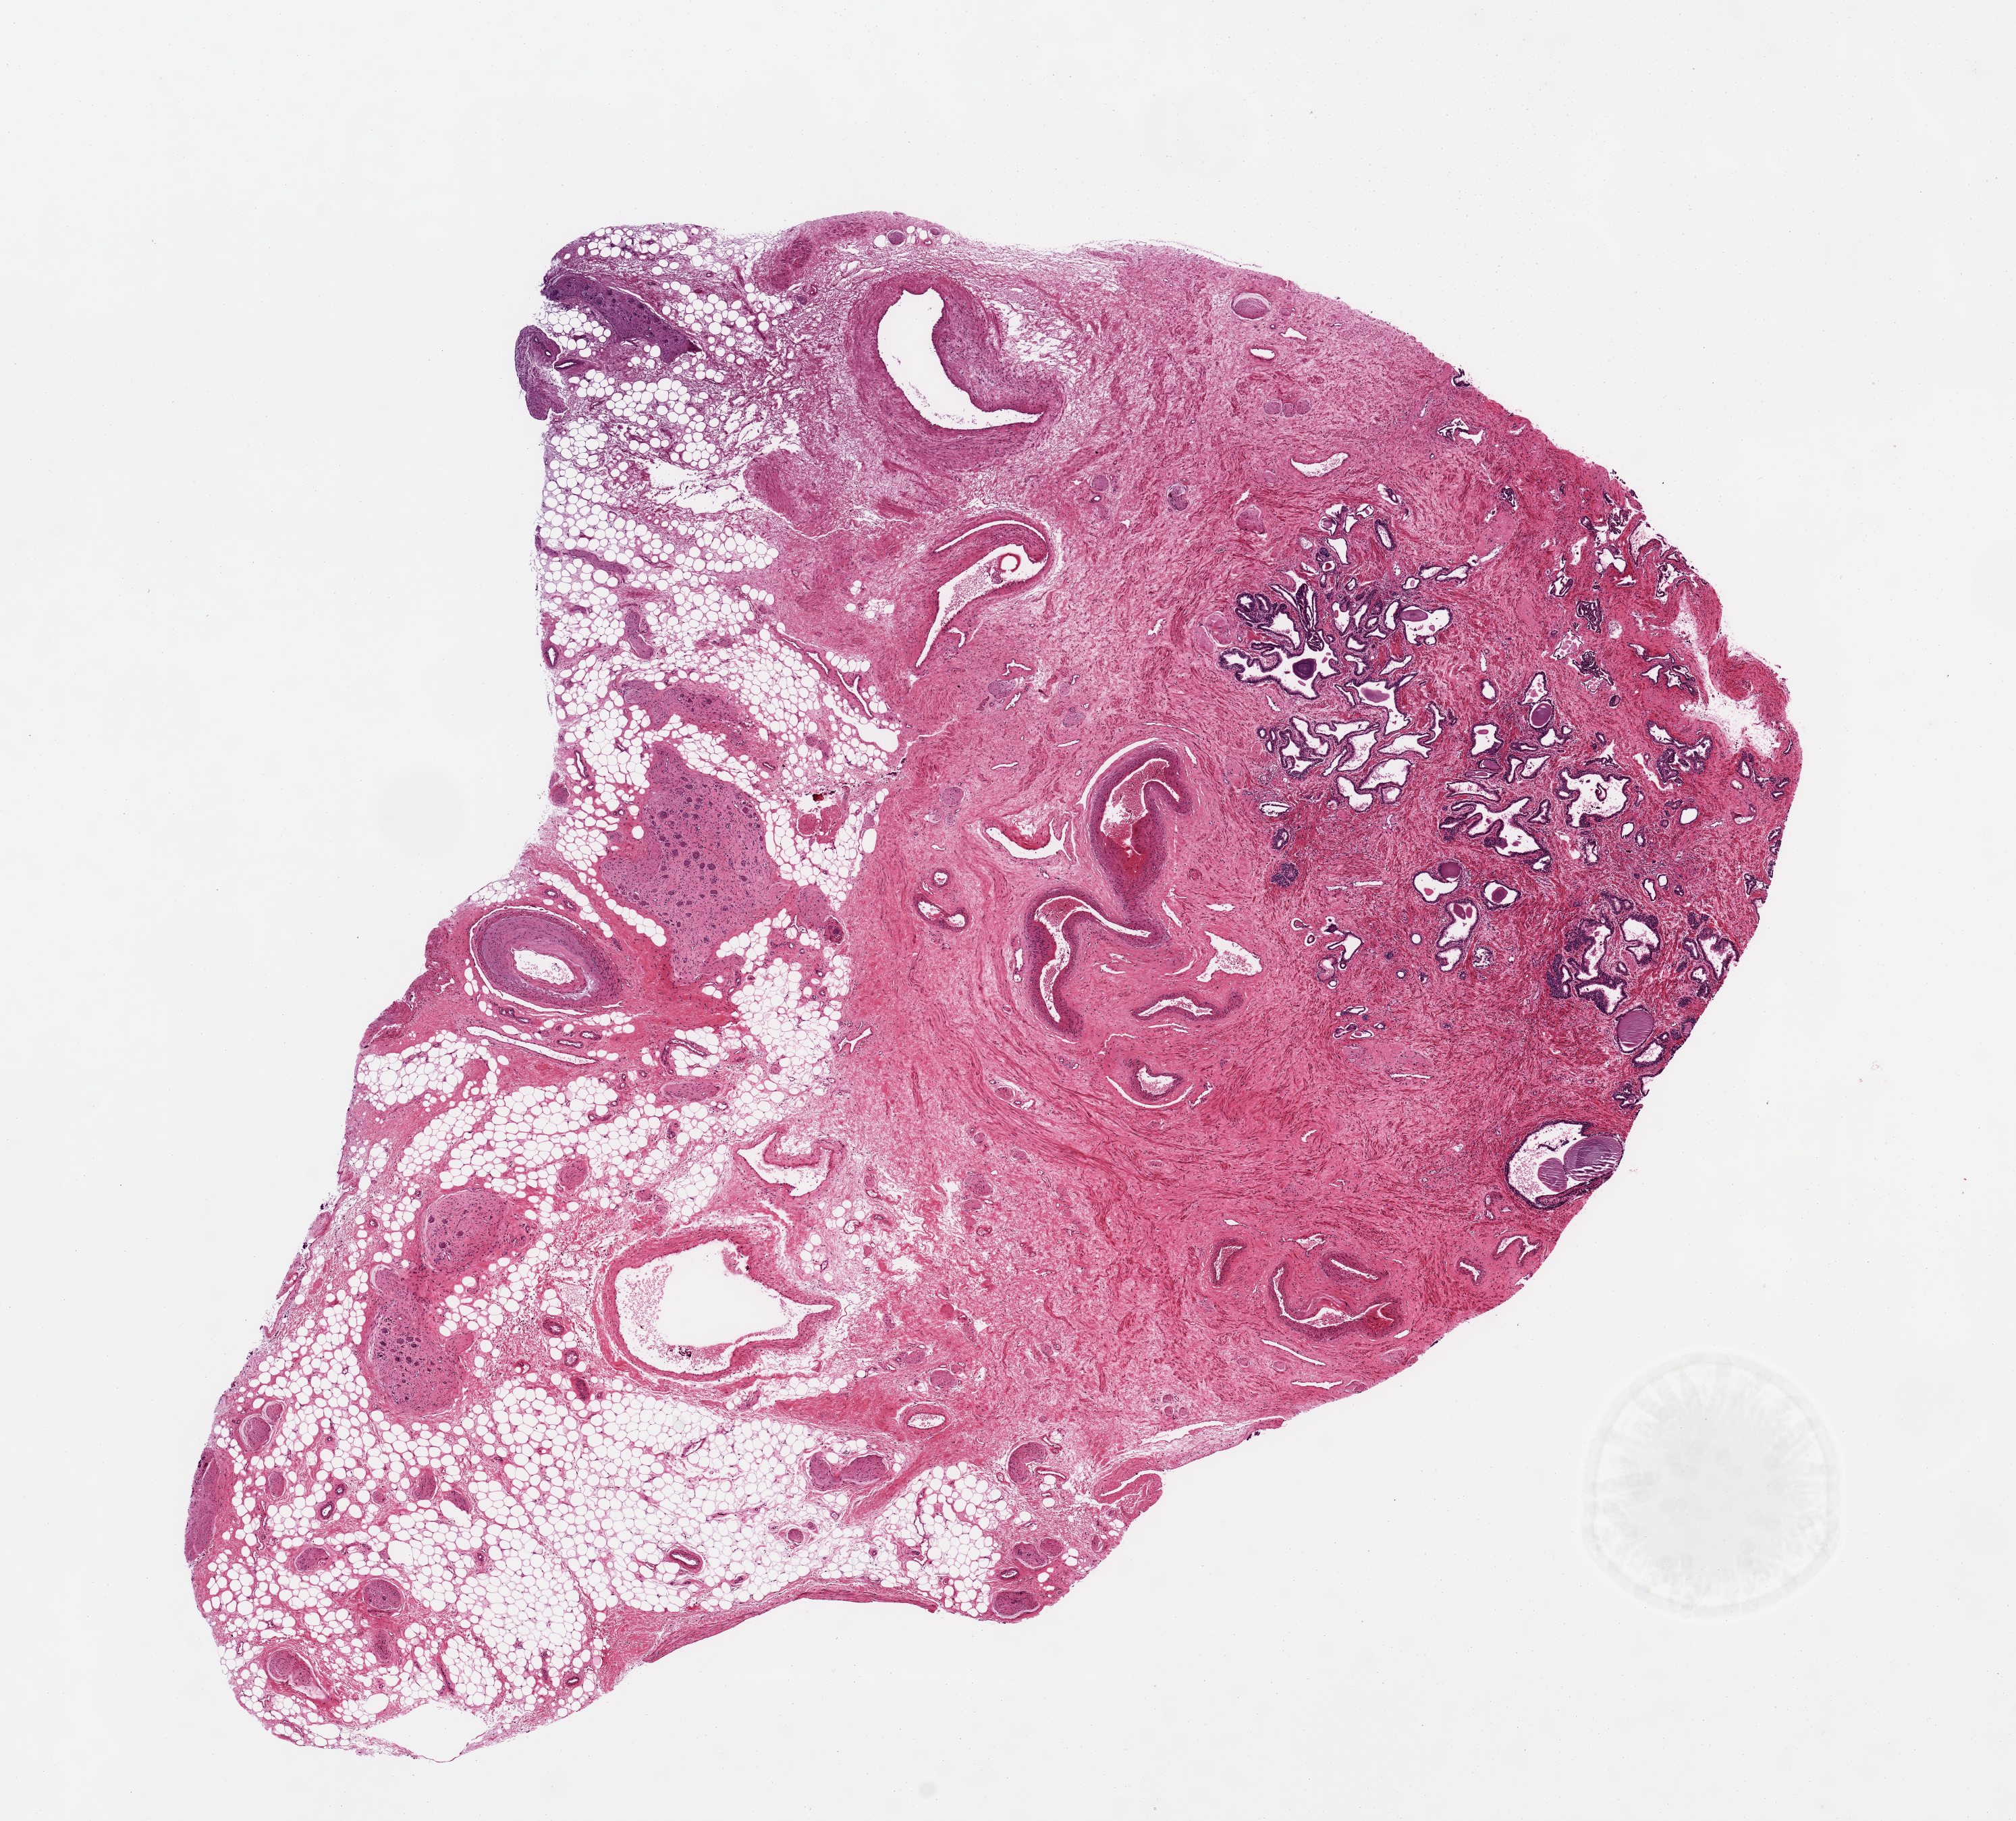
Whole-slide image, H&E stain, a low-resolution overview of the entire scanned area, about 11.8 x 10.7 mm (from a 20x scan), PAXgene-fixed paraffin-embedded (PFPE) section, section of prostate (target tissue), donor tissue sample. Donor: male.
Pathologist's review note for this sample: Glandular component is approximately 20% of specimen.